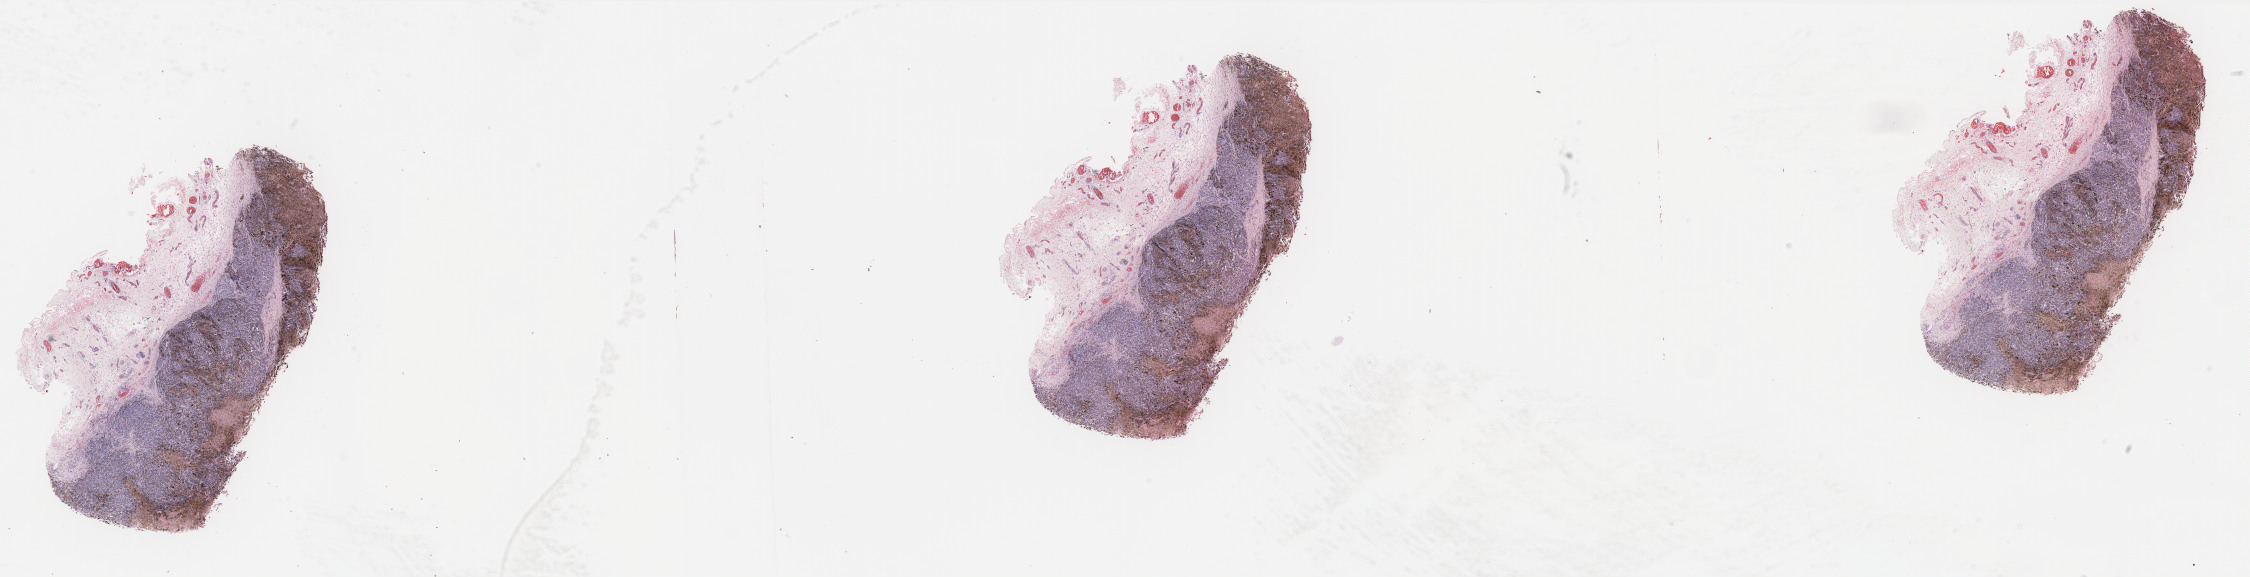
Whole-slide histology image, H&E-stained — a low-resolution overview of the entire scanned area, about 36.1 x 9.3 mm (slide scanned at 40x). Formalin-fixed paraffin-embedded (FFPE) diagnostic section. Skin, primary tumour sample. Male, age 63 years at initial diagnosis.
Pathologic diagnosis: Malignant melanoma, NOS.